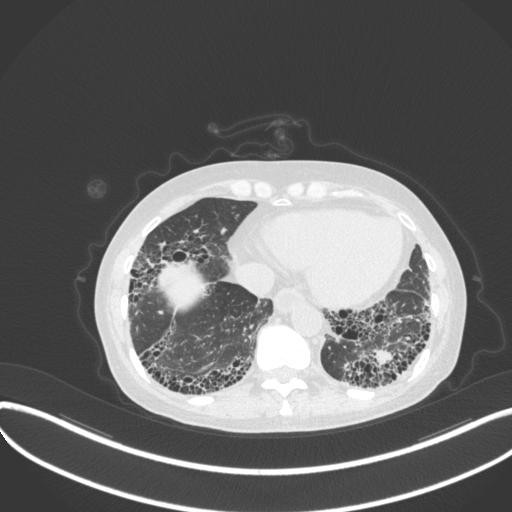
Chest CT, one axial slice. Slice 75 of 373 in the series (ordered by position). Lung window (W 1500 / L -600 HU). 512 × 512 image matrix. Patient: female, 56 years. From the clinical record (not read from this slice): clinical TNM (as recorded): T1 N0 M0.
Outlined on this slice (bounding box drawn by a radiologist):
- lung tumour (recorded histology: adenocarcinoma): box from (x=371, y=348) to (x=403, y=371) px